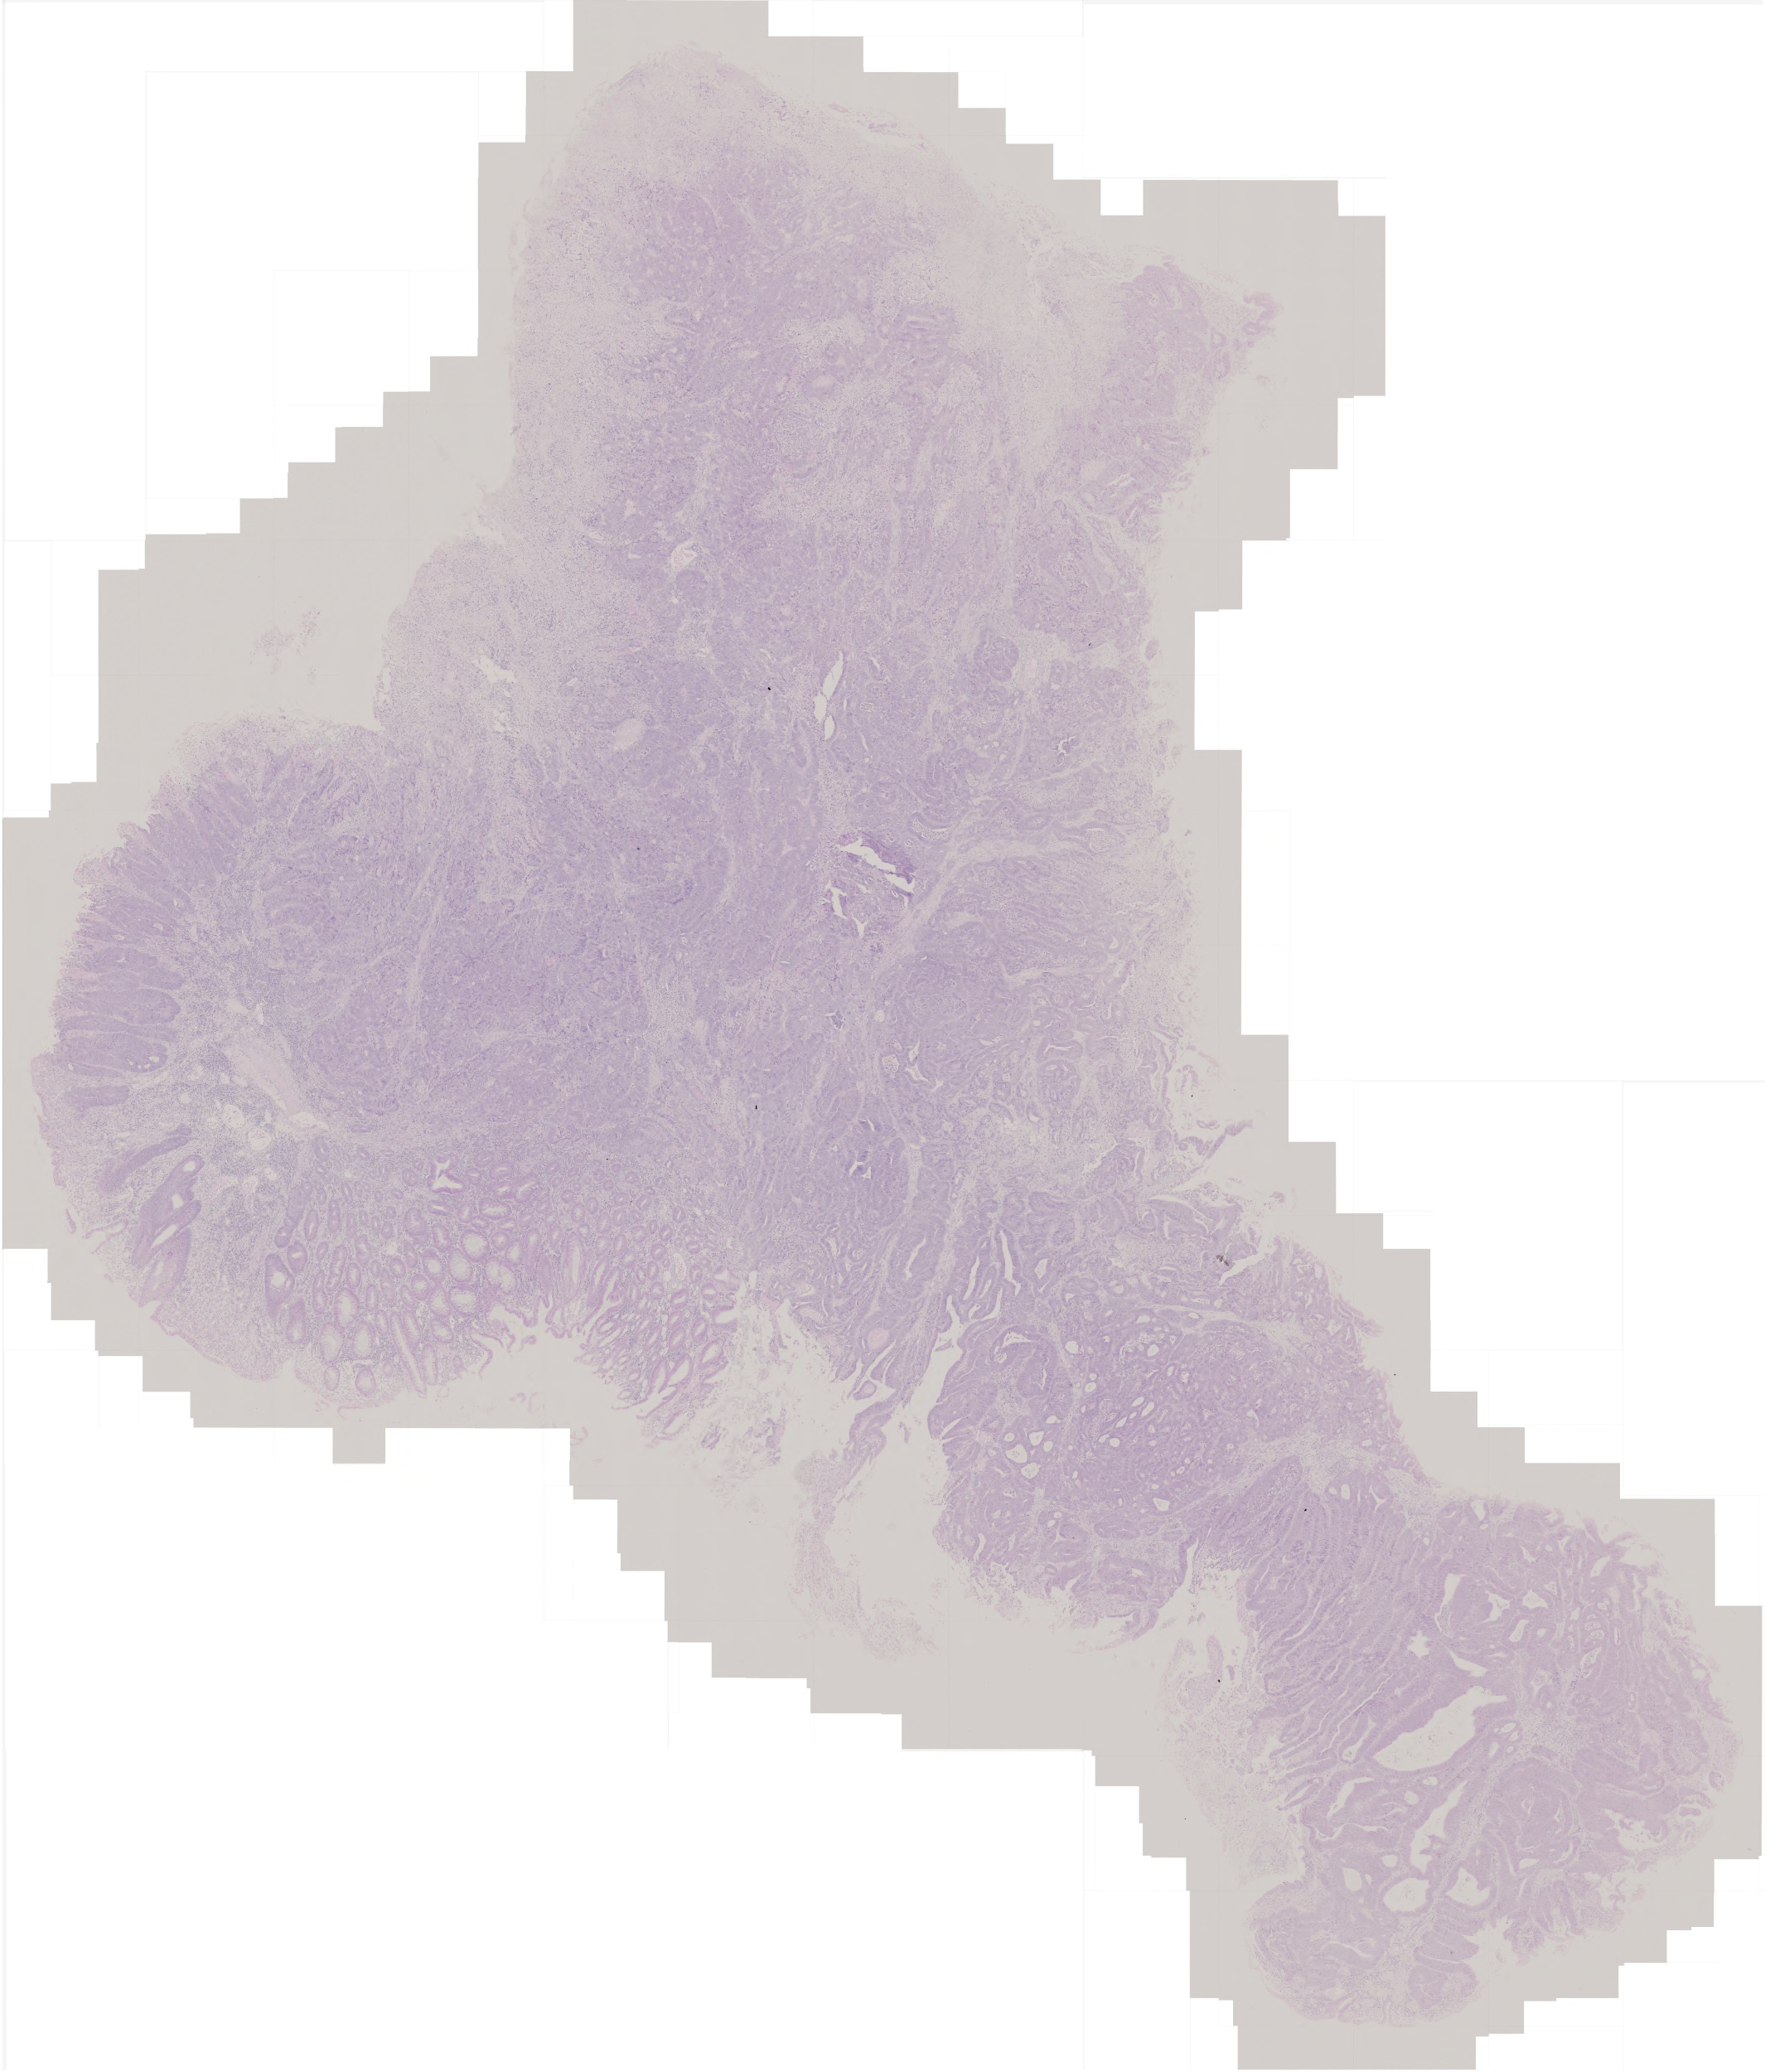
Whole-slide histology image, H&E-stained — whole scanned area (about 4.3 x 5.0 mm) shown as a low-resolution overview, formalin-fixed paraffin-embedded (FFPE) diagnostic section, colon, primary tumour sample. Male patient; age at initial diagnosis 70 years.
Histologic diagnosis: Adenocarcinoma, NOS (ascending colon).